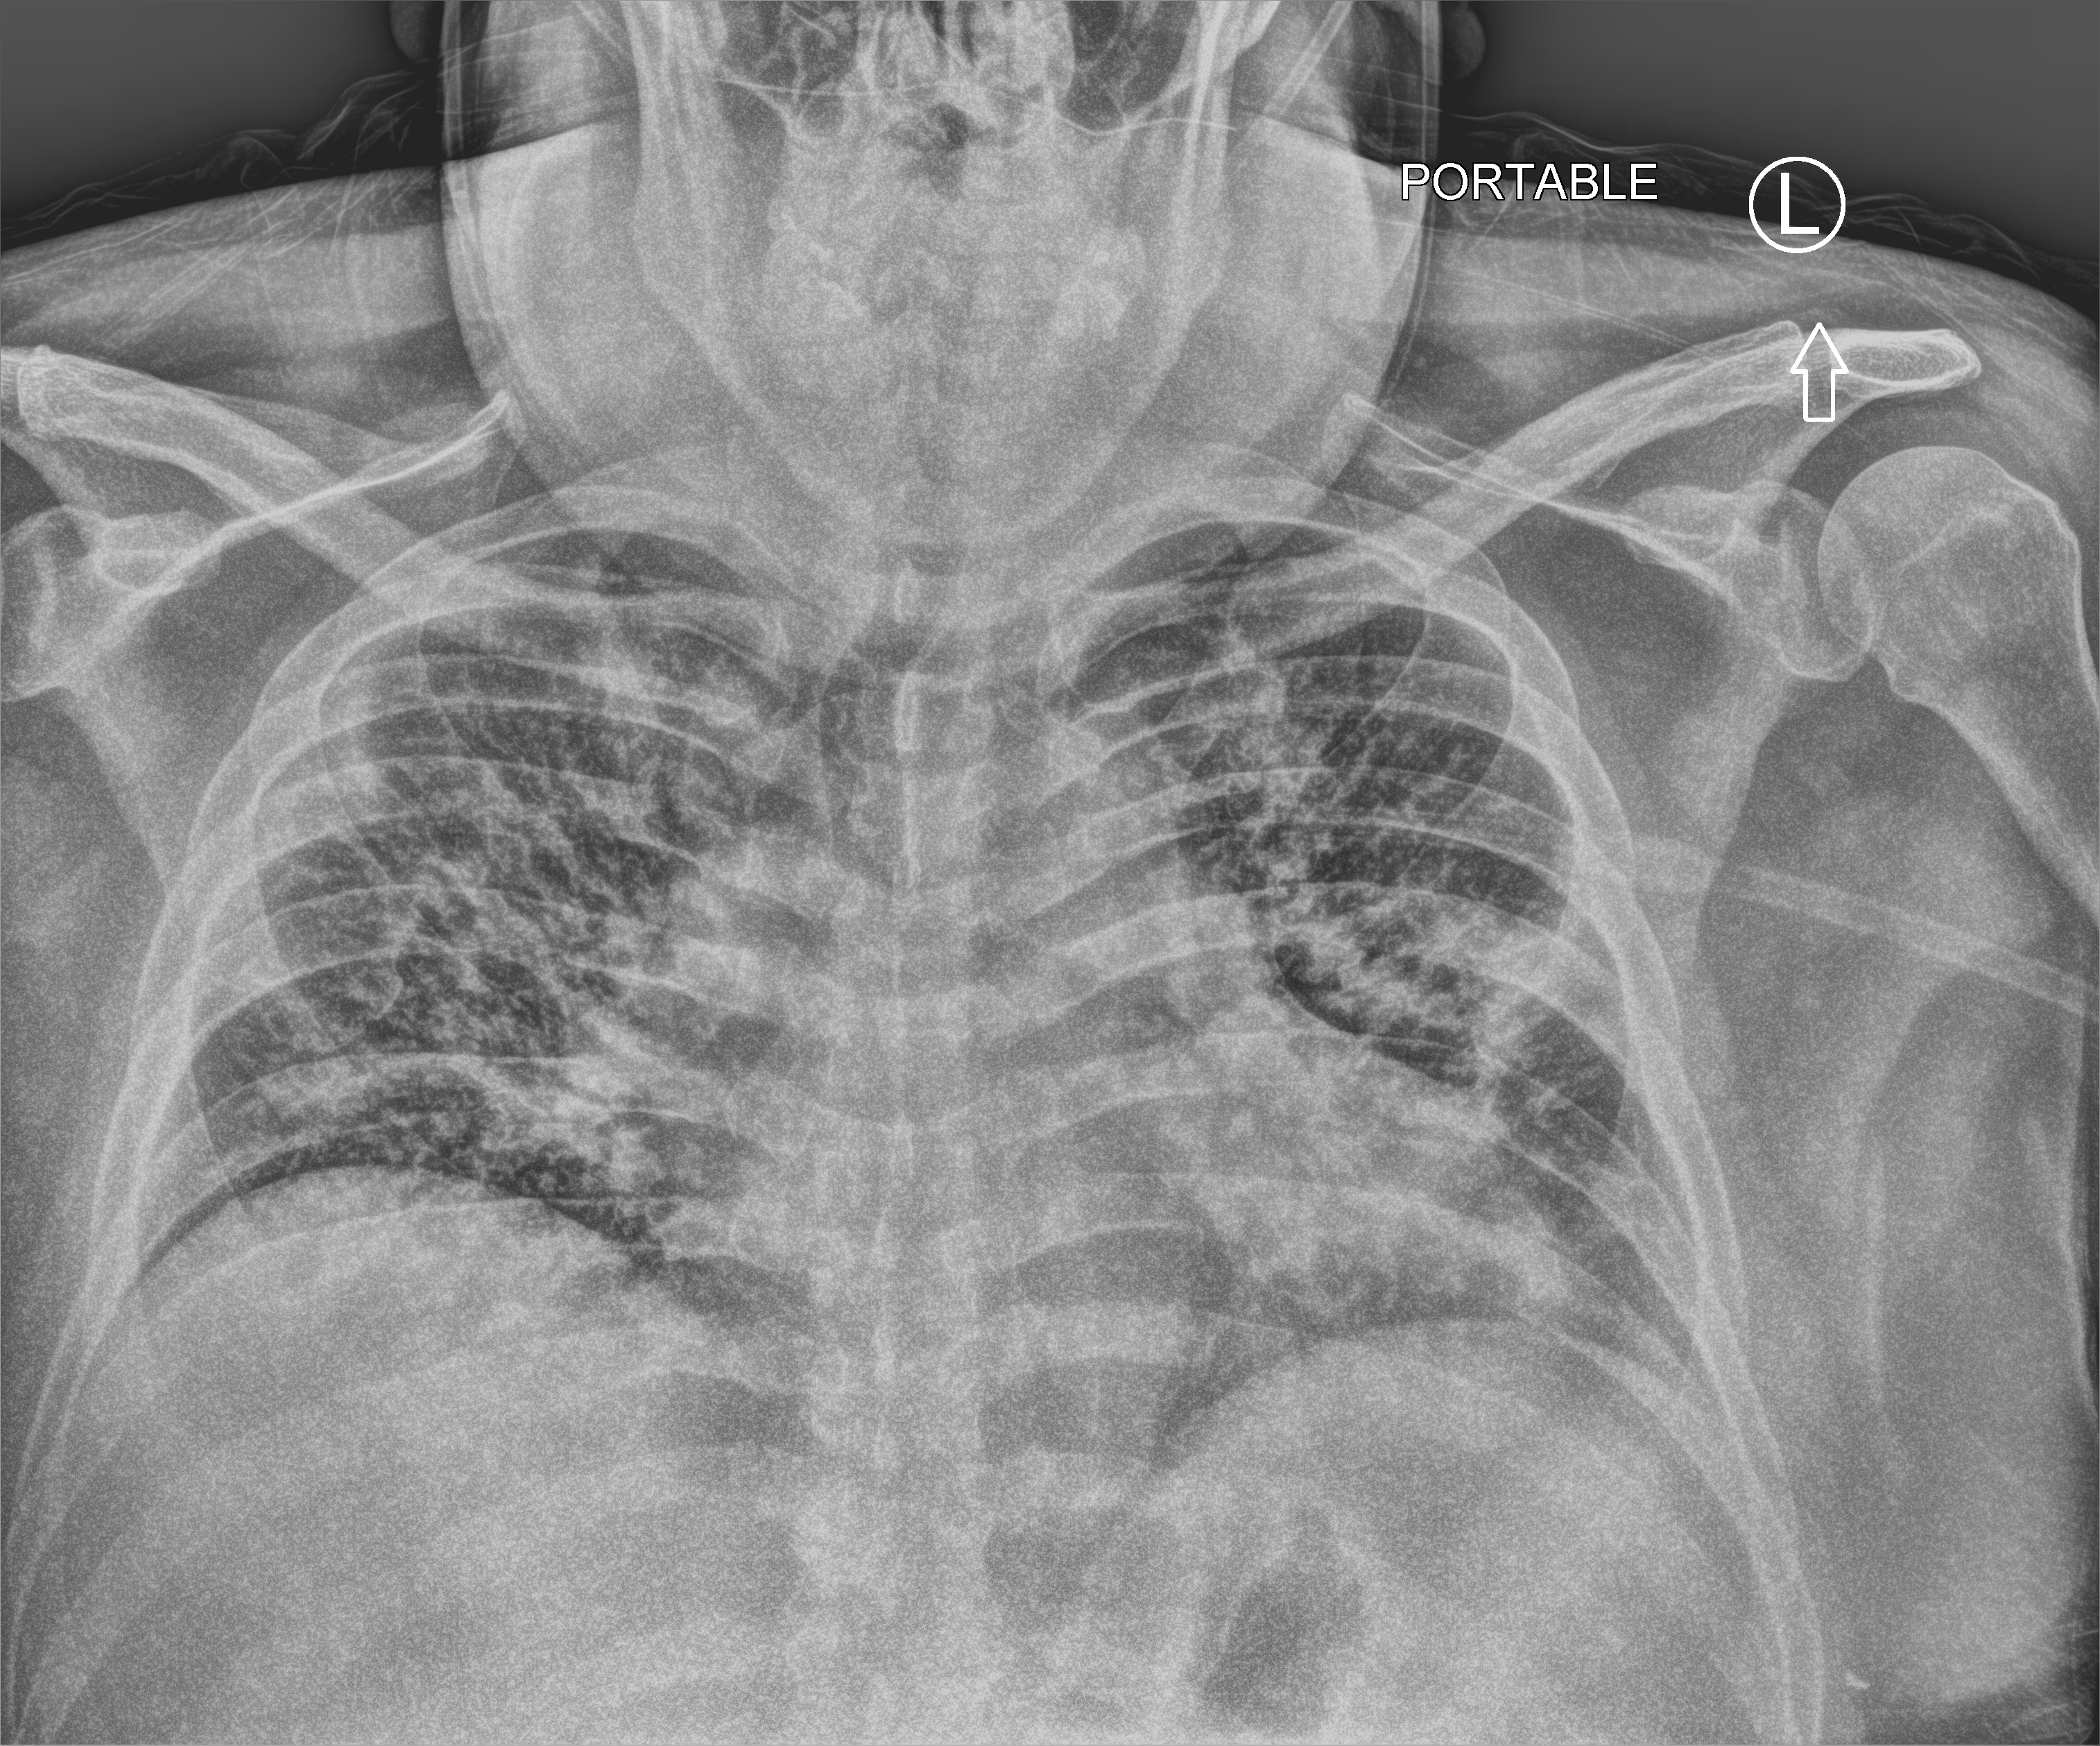
Chest X-ray (portable); anteroposterior (AP) projection. Patient hospitalised with COVID-19; male, aged 18–59 years.
Hospital-stay facts (about this admission, not read from this image; timing relative to this image not recorded):
- admitted to intensive care during this hospital stay: no
- mechanically ventilated during this hospital stay: no